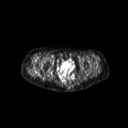
FDG PET of an extremity soft-tissue mass (from a PET/CT study), one axial slice. Slice 53 of 267 in the series (ordered by position). 3.27 mm slice thickness. 128 × 128 image matrix. Patient: female, 57 years. From the clinical record (not read from this slice): histological type: epithelioid sarcoma with vascular differentiation; site of the primary tumour: right buttock.
Structures marked on this image (expert contour drawn on MRI and transferred to this co-registered scan by the dataset authors):
- gross tumour volume (mass): bounding box (x1, y1, x2, y2) in pixels: (26, 66, 40, 78)